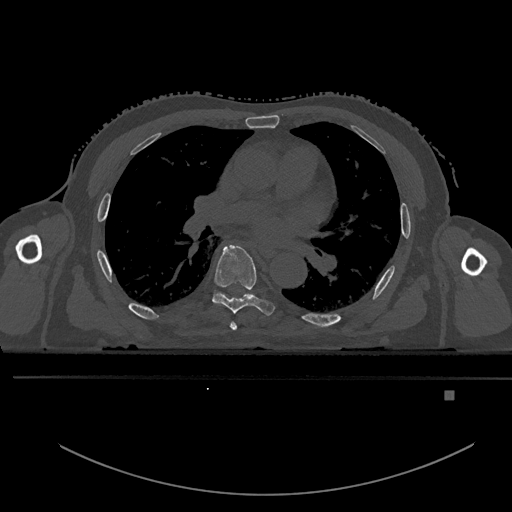
CT including the spine, one axial slice; position 306 of 969 along the scan axis; bone window (W 1800 / L 400 HU); 512 × 512 image matrix, field of view 456 × 456 mm. Male patient, age 82 years. Case-level facts recorded for this patient, not image findings: primary cancer: prostate.
Annotated regions visible in this slice (semi-automatically segmented with operator editing):
- T5 vertebra: bounding box [x1, y1, x2, y2] px = [230, 321, 237, 331]
- T6 vertebra: [212, 245, 275, 316]